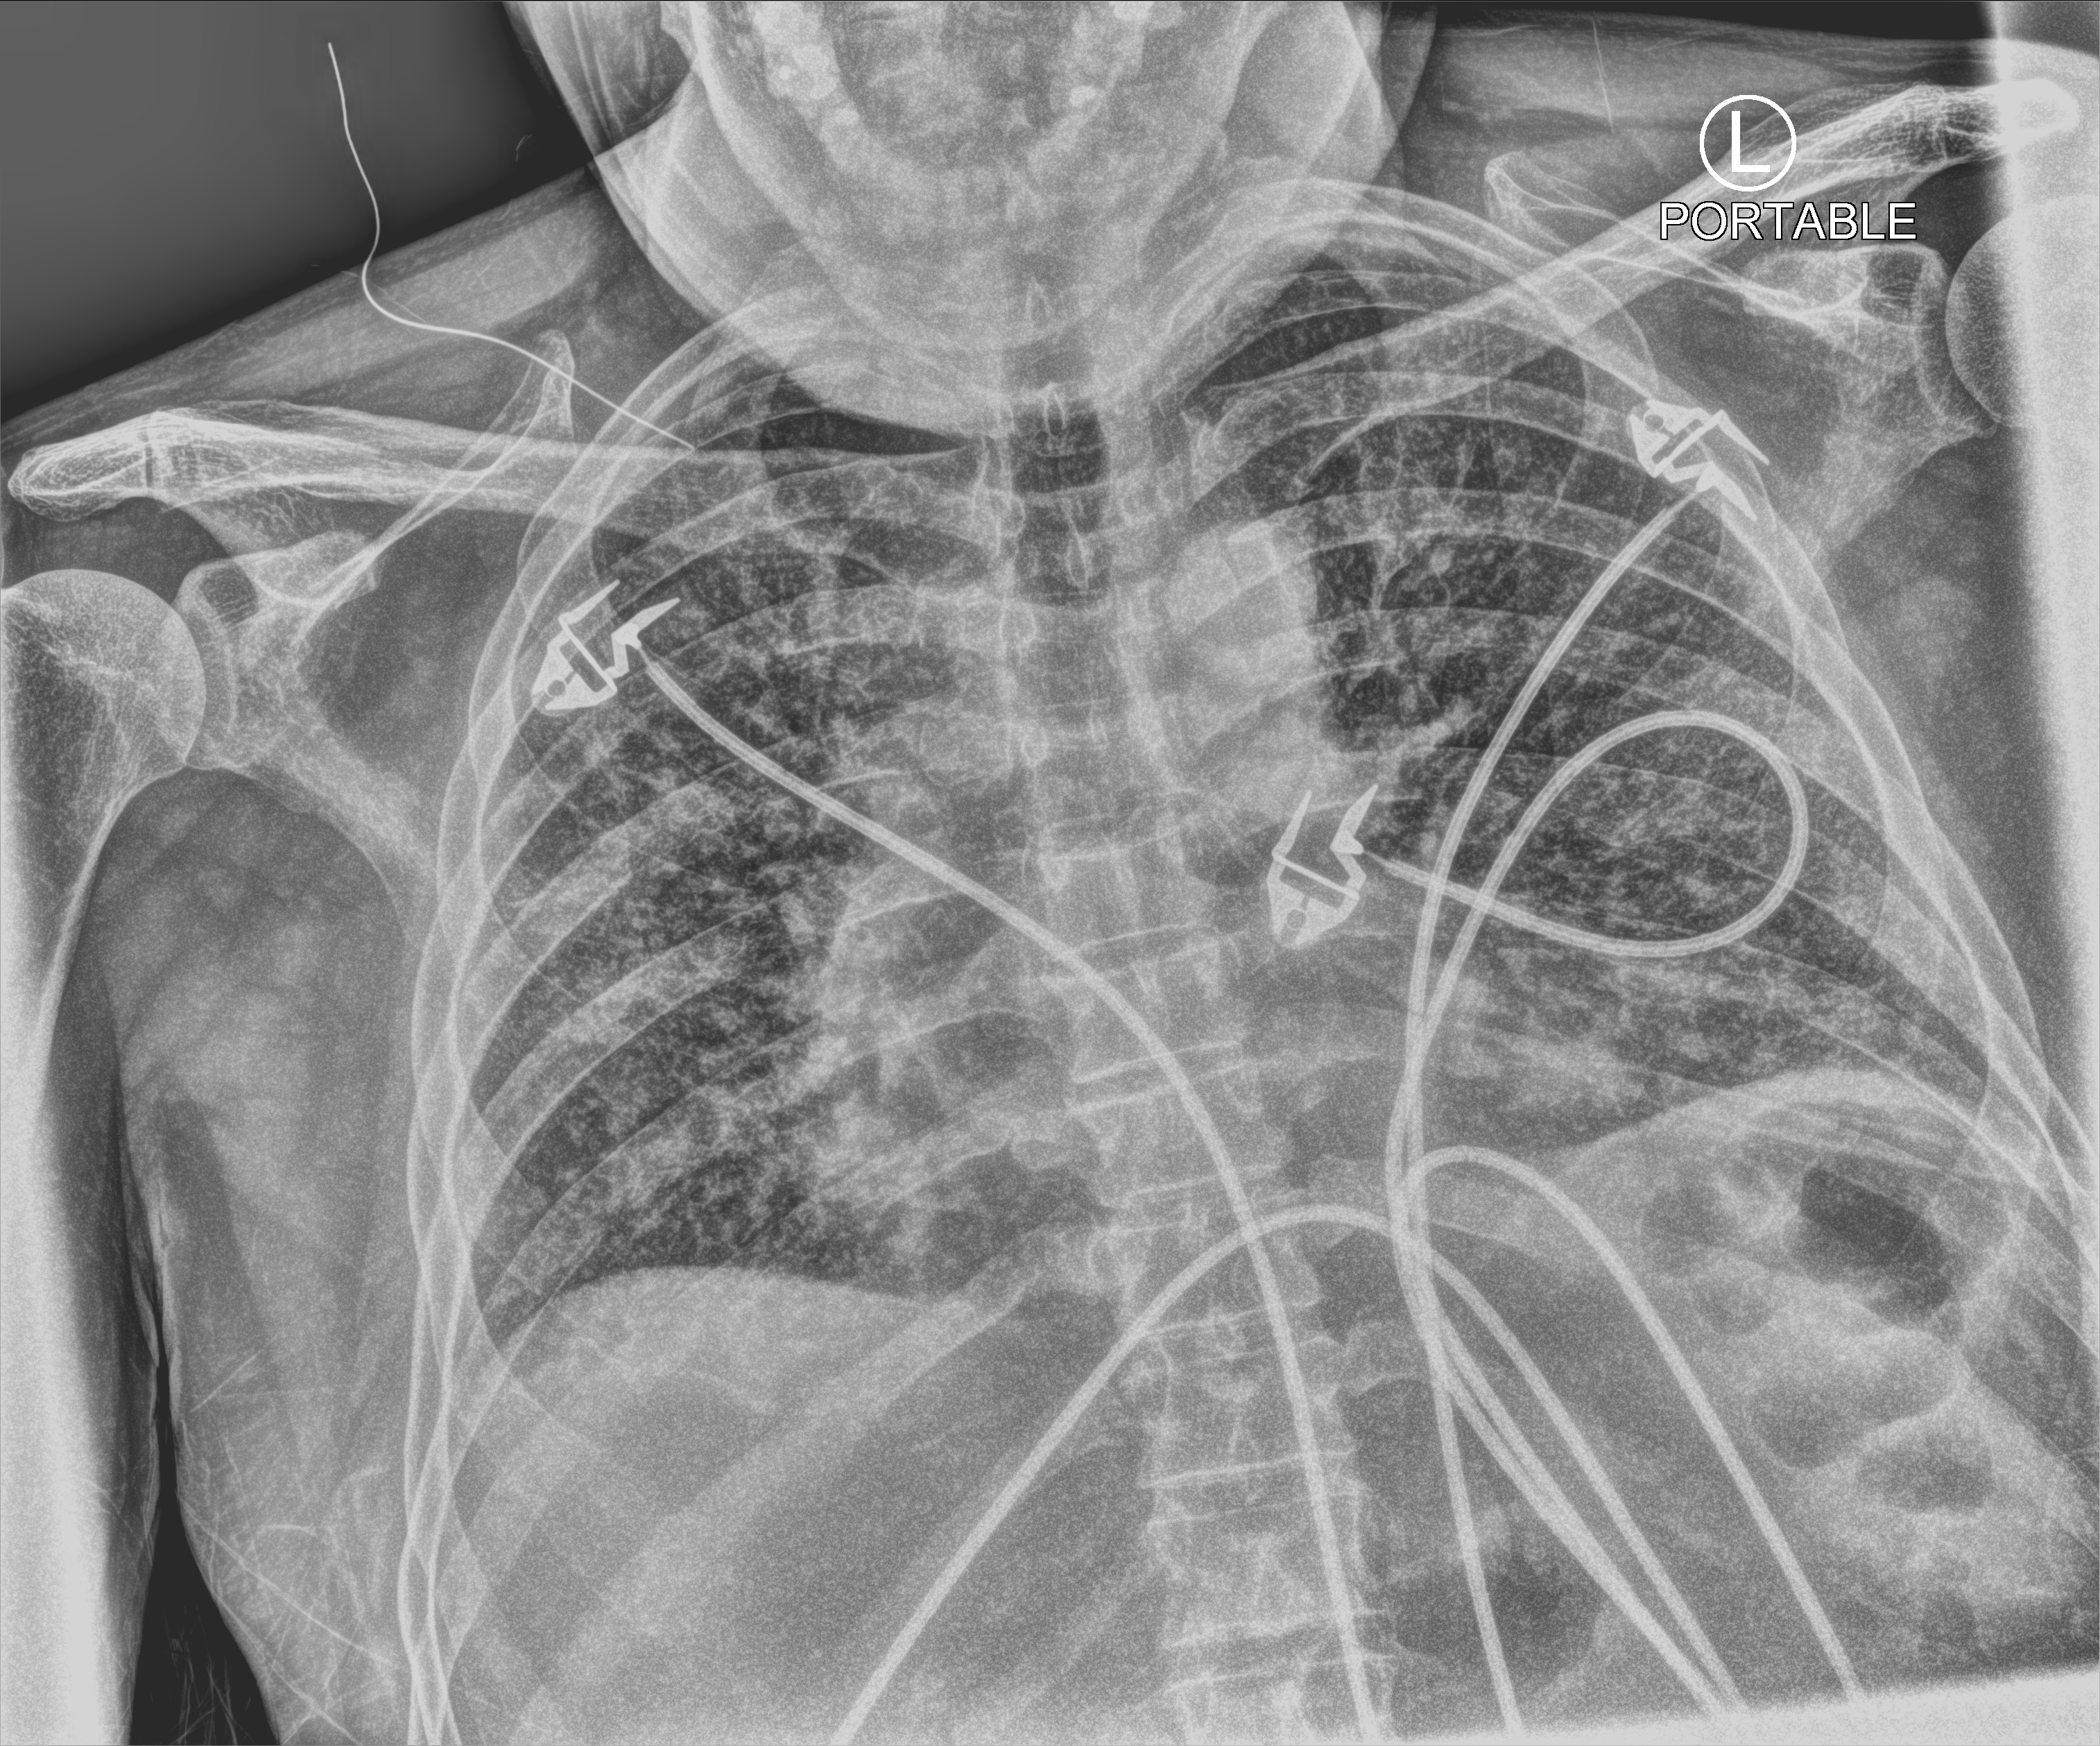
Bedside chest radiograph (computed radiography), anteroposterior (AP) projection. Male patient hospitalised with COVID-19, age 60–74 years.
Admission-level facts for this patient (not findings on this image; timing relative to this image not recorded): mechanically ventilated during this hospital stay: yes; admitted to intensive care during this hospital stay: yes.